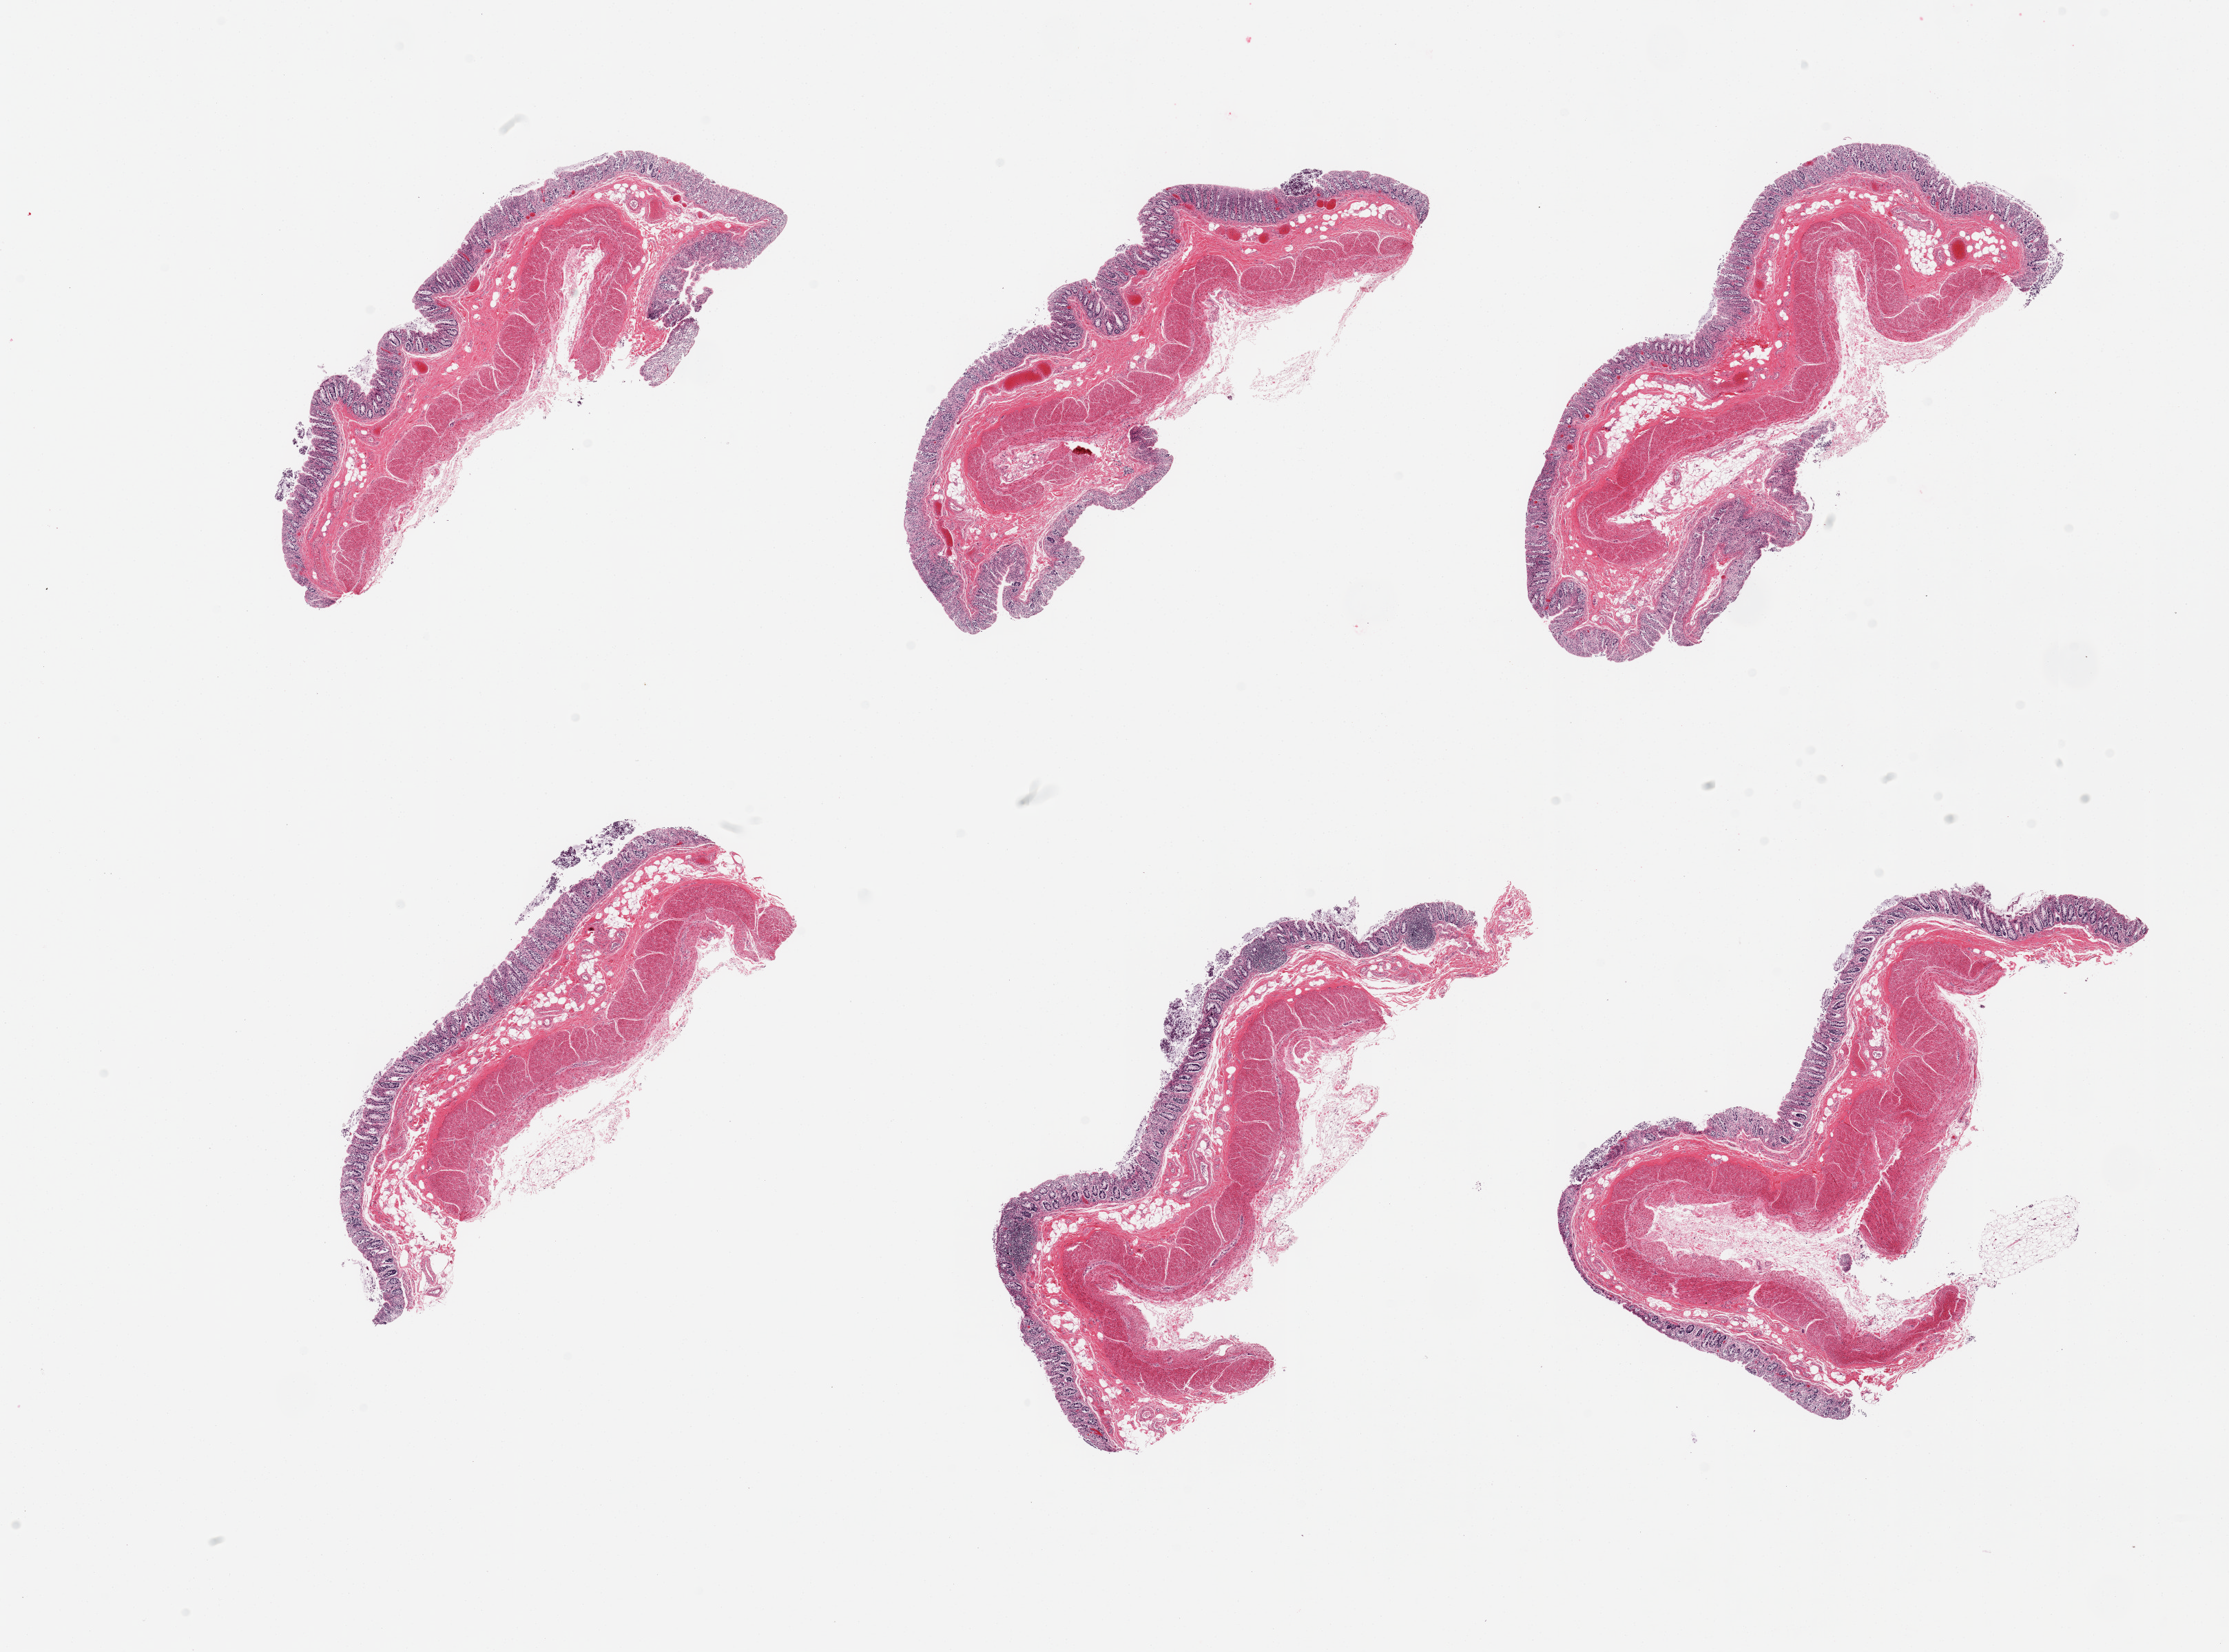
Whole-slide image, haematoxylin and eosin stain, brightfield, a low-resolution overview of the entire scanned area, about 25.6 x 19.0 mm. PAXgene-fixed, paraffin-embedded tissue. Section of transverse colon (target tissue). Donor tissue sample. Donor sex: male.
* reviewer comment on this tissue sample: 6 pieces mucosa ~ 0.3mm, ~15-20% thickness, but markedly autolyzed glands, largely lamina propria remains